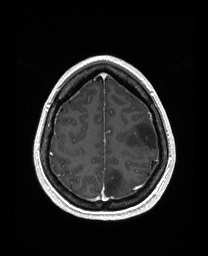
Brain MRI from a brain-tumour surgery series, one axial slice. Slice 127 of 176 in the series (ordered by position). T1-weighted post-contrast. 1 mm slice thickness. 208 × 256 image matrix, field of view 203 × 250 mm. Case-level facts recorded for this patient, not image findings: histopathology: Astrocytoma; WHO grade: 3; IDH mutation: yes.
Structures marked on this image (outlined manually by an expert reader):
- tumour: box from (x=126, y=119) to (x=158, y=150) px